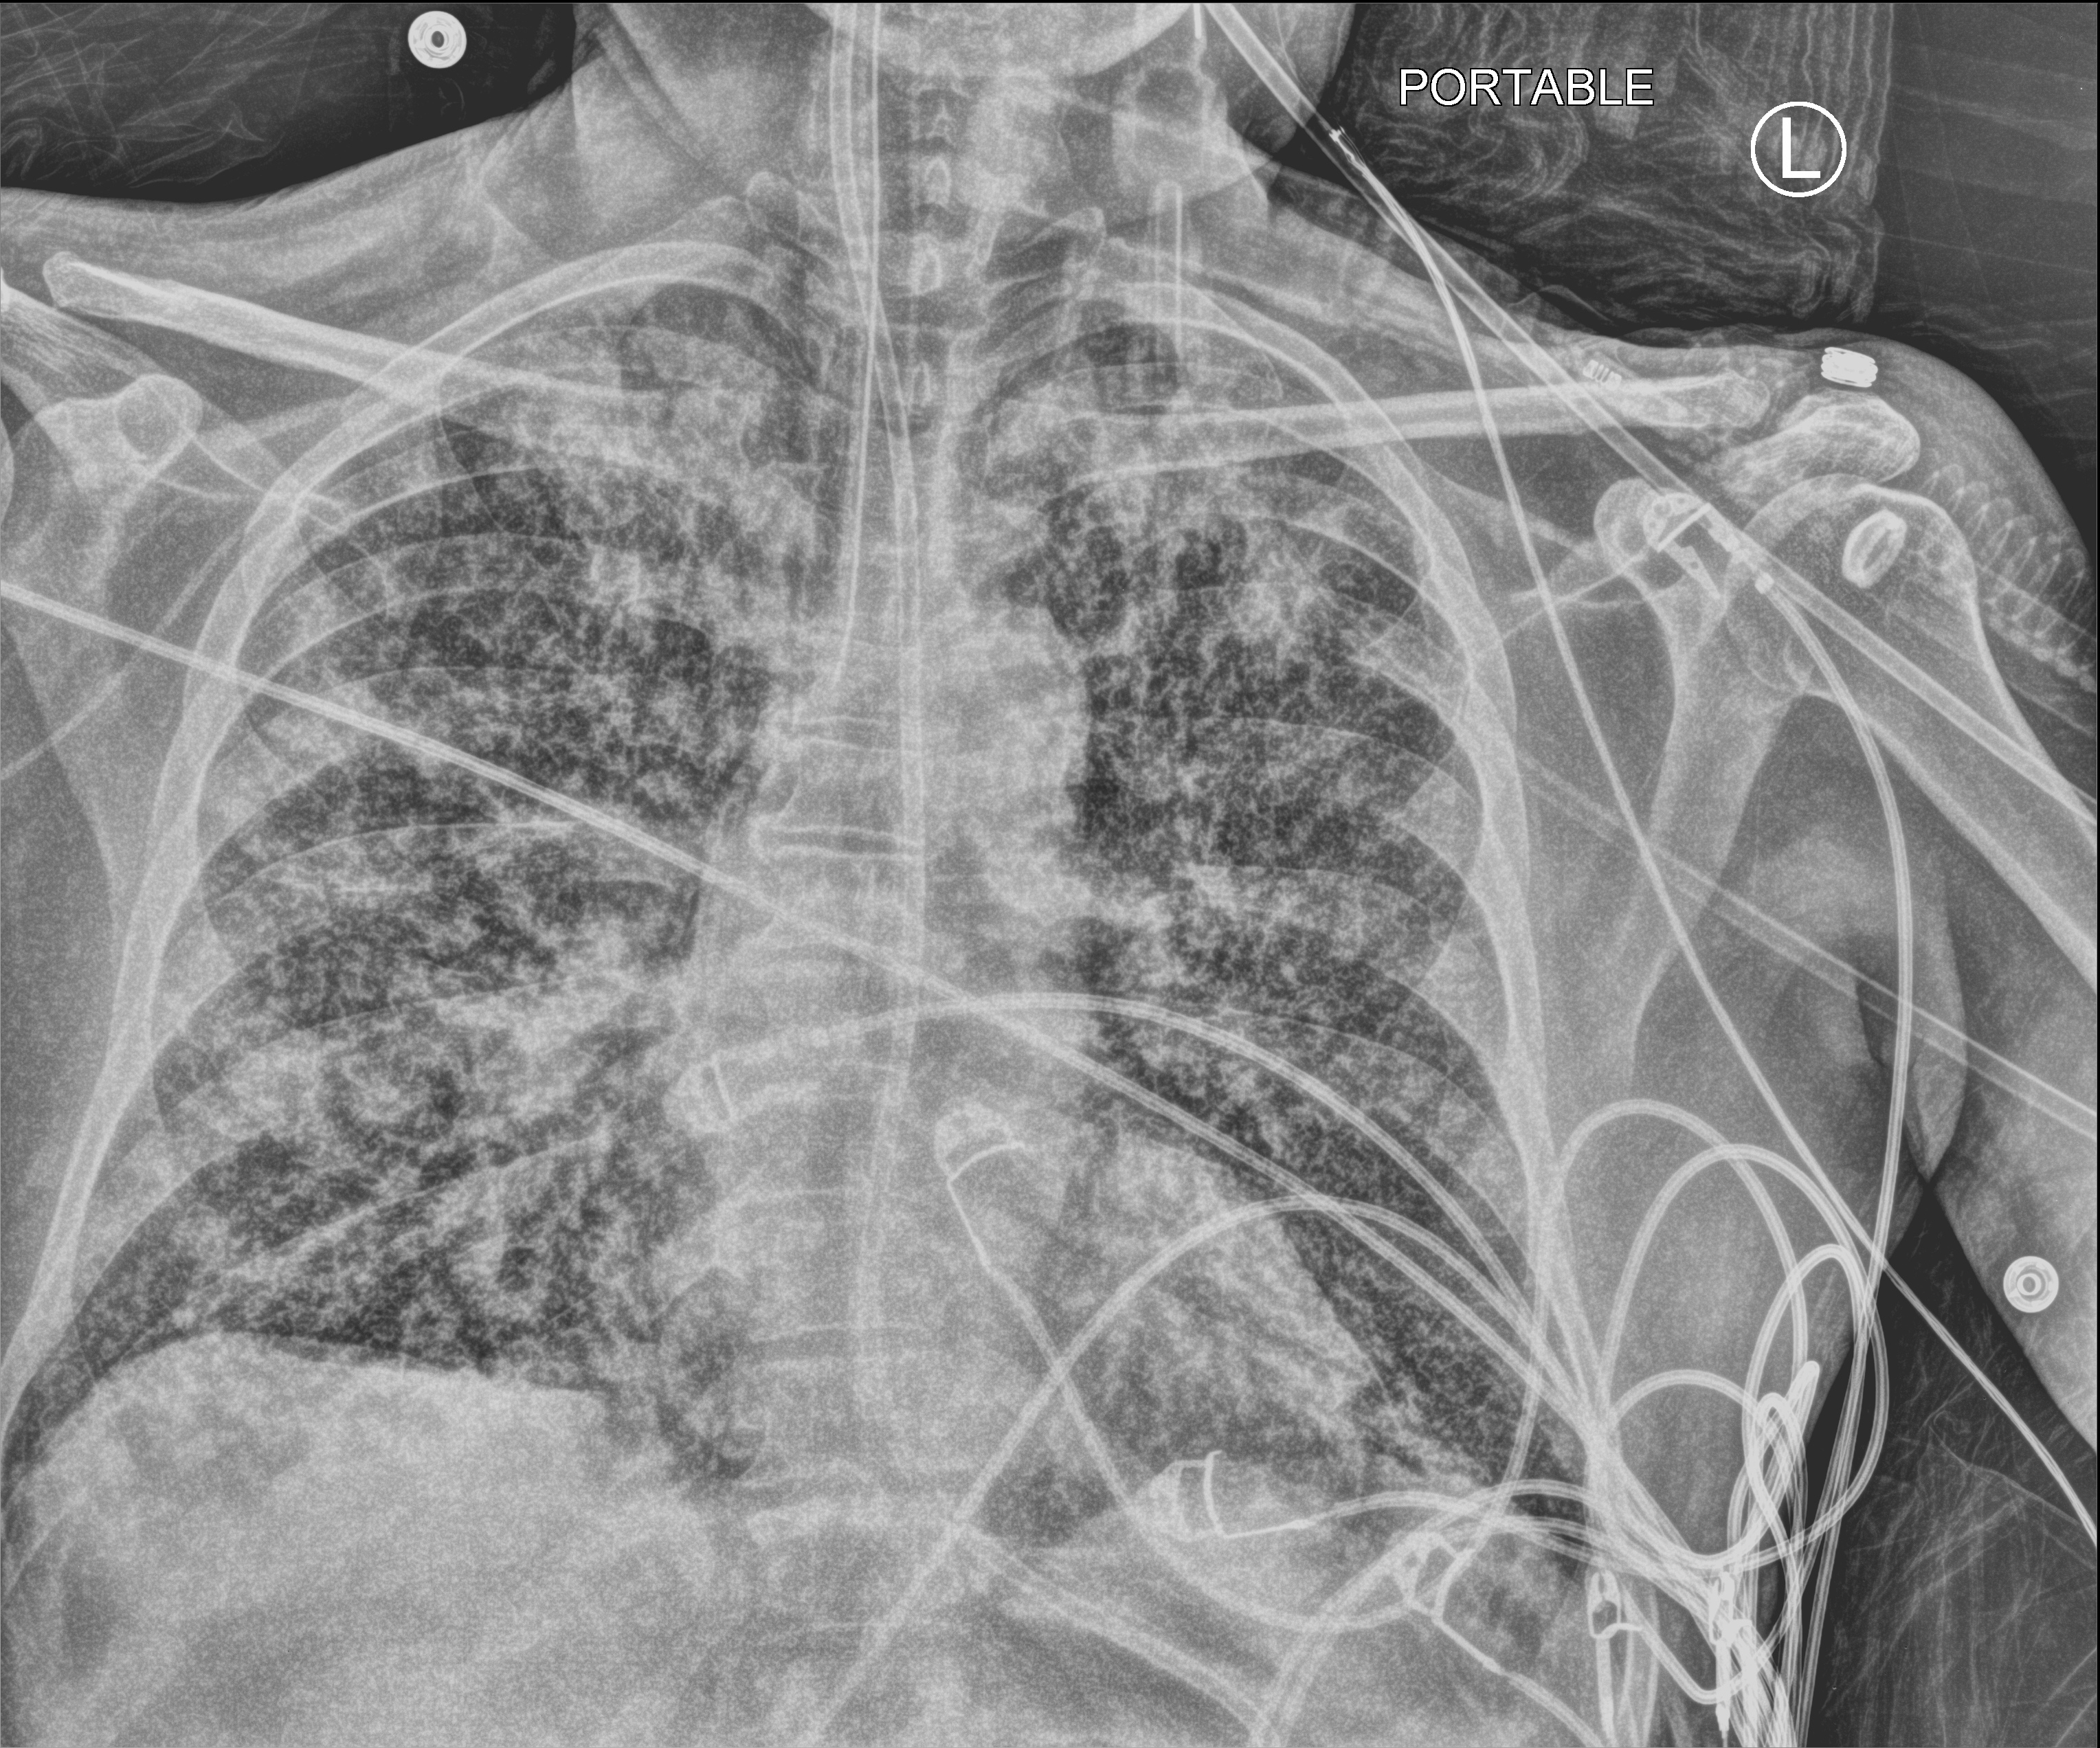
Bedside chest radiograph (computed radiography), anteroposterior (AP) projection. Patient hospitalised with COVID-19; male, aged 18–59 years.
From the hospital-stay record, not from the radiograph (when in the stay this image was taken is not recorded): smoking status (admission record): never; hypertension (admission record): no; admitted to intensive care during this hospital stay: yes.